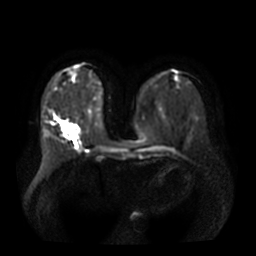
Breast MRI, one axial slice; position 14 of 36 along the scan axis; diffusion-weighted series; image 2 of 4 stored at this slice position (different b-values; order by instance number); 3 T; 256 × 256 image matrix. Female patient.
Annotated regions visible in this slice (outlined manually by an expert reader):
- tumour on diffusion-weighted imaging: bounding box <59,123,77,139> (left, top, right, bottom; pixels)